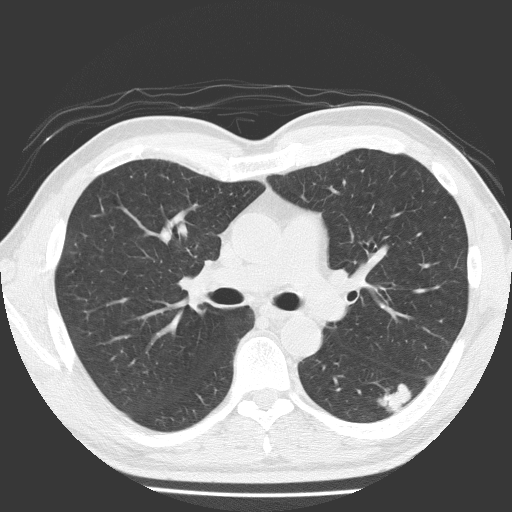
Chest CT (low-dose screening protocol), one axial image, first (baseline) screen, lung window (W 1500 / L -600 HU), lung (sharp) reconstruction kernel (FC51), slice 74 of 184 in the series, 512 × 512 image matrix, field of view 348 × 348 mm. Male participant, aged 58 years at enrolment.
Lesion marked by an expert reader, bounding box <371,374,425,423> (left, top, right, bottom; pixels). The screening reader recorded 4 non-calcified nodules or masses ≥4 mm on this exam (left lower lobe, left lower lobe, right middle lobe, left upper lobe); which of them this box marks is not recorded. Official screen result: positive, change unspecified: nodule(s) >= 4 mm or enlarging nodule(s), mass(es), or other non-specific abnormalities suspicious for lung cancer. Participant outcome: lung cancer diagnosed 99 days after this screen — adenosquamous carcinoma, left lower lobe, moderately differentiated (G2), stage IA (AJCC 6th edition), 28 mm at pathology.